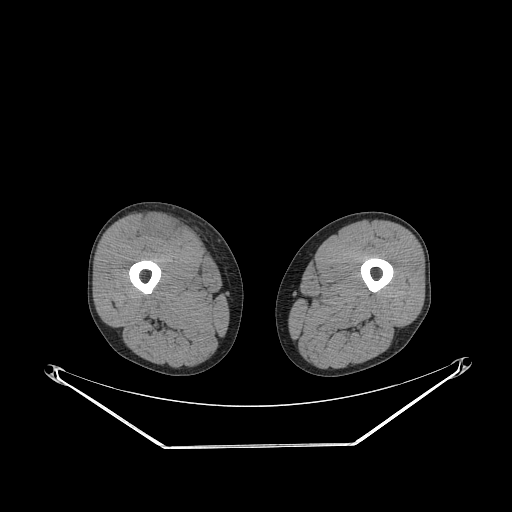
CT of an extremity soft-tissue mass (from a PET/CT study), one axial slice. Position 248 of 311 along the scan axis. 140 kVp. Soft-tissue window (W 400 / L 40 HU). 3.75 mm slice thickness. 512 × 512 image matrix, field of view 500 × 500 mm. Male patient. From the clinical record (not read from this slice): histological type: pleiomorphic leiomyosarcoma; grade: intermediate; site of the primary tumour: right thigh.
Structures marked on this image (expert contour drawn on MRI and transferred to this co-registered scan by the dataset authors):
- gross tumour volume including surrounding oedema: bounding box (x1, y1, x2, y2) in pixels: (144, 215, 181, 243)